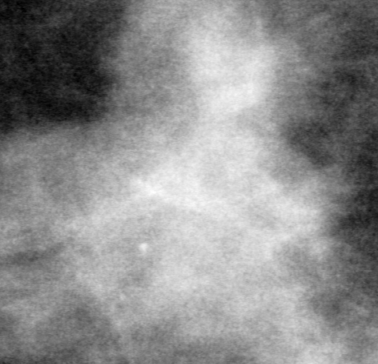
Crop from a digitized film mammogram around one marked abnormality; left breast; CC view.
Mass, shape irregular, margins ill defined; BI-RADS assessment category 4; pathology result (as recorded, not read from the image): malignant.